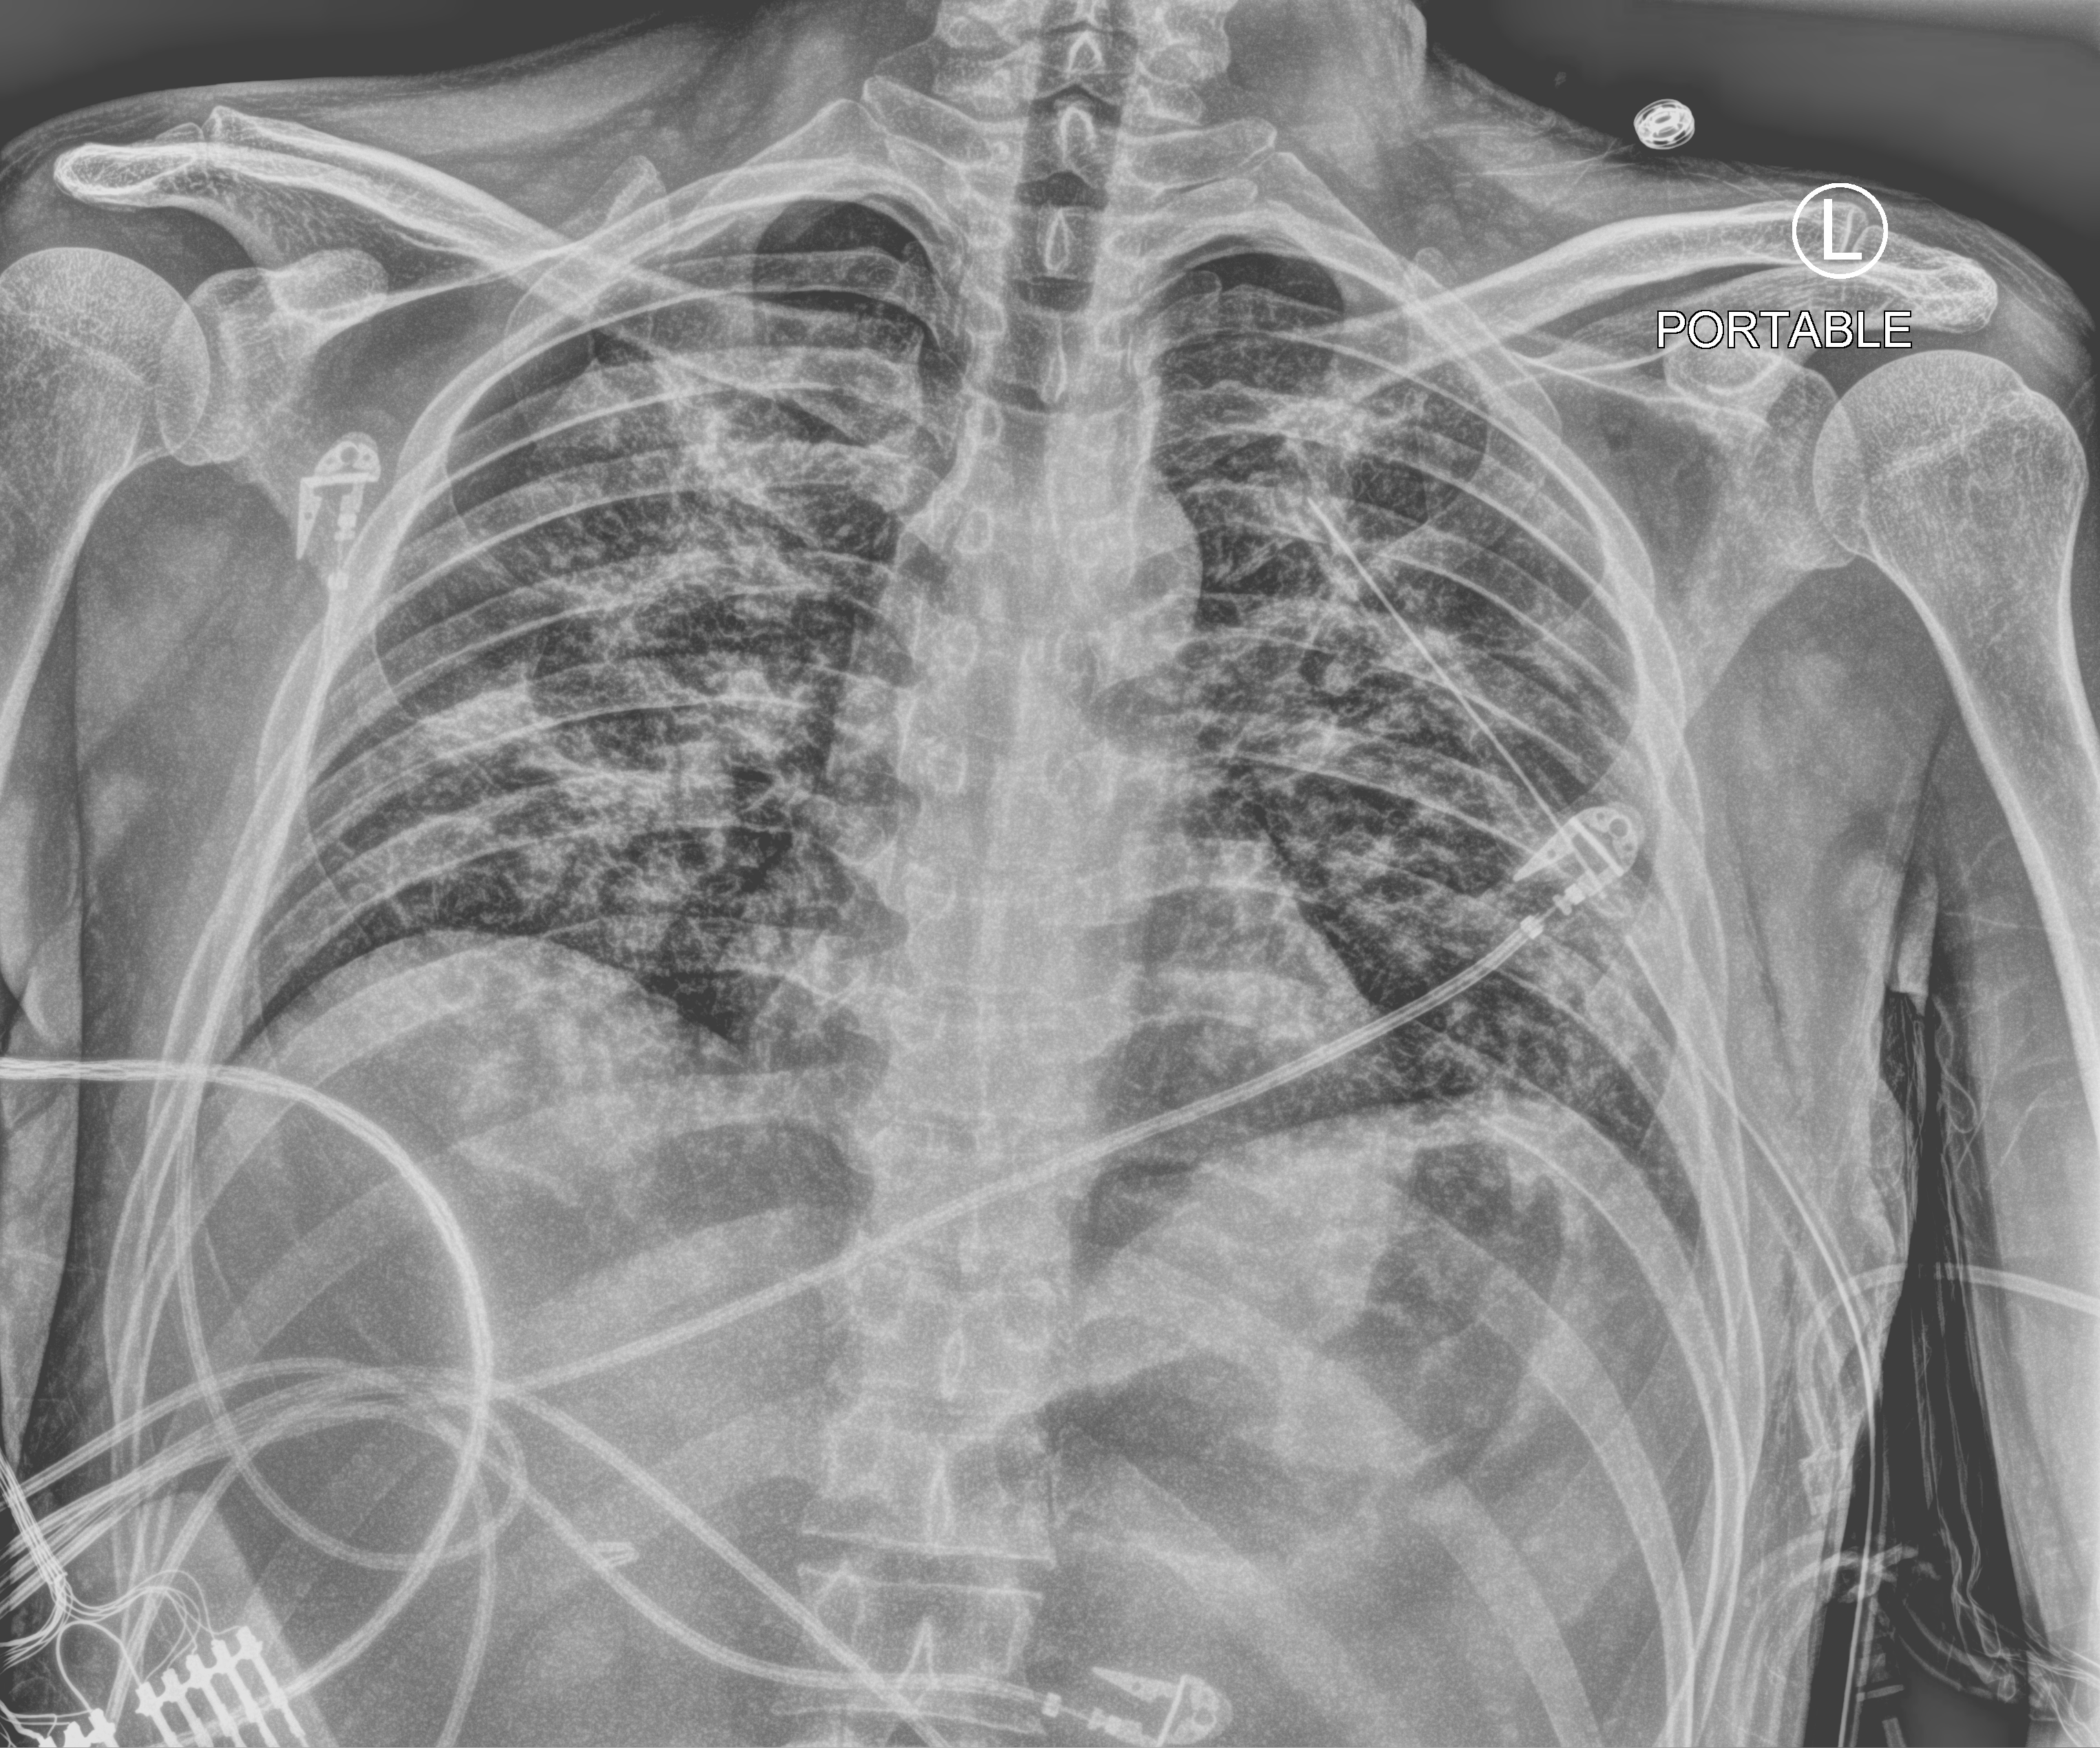
Bedside chest radiograph (computed radiography), anteroposterior (AP) projection. Male patient hospitalised with COVID-19, age 18–59 years.
Hospital-stay facts (about this admission, not read from this image; timing relative to this image not recorded): mechanically ventilated during this hospital stay: yes; chronic kidney disease (admission record): no; admitted to intensive care during this hospital stay: yes.